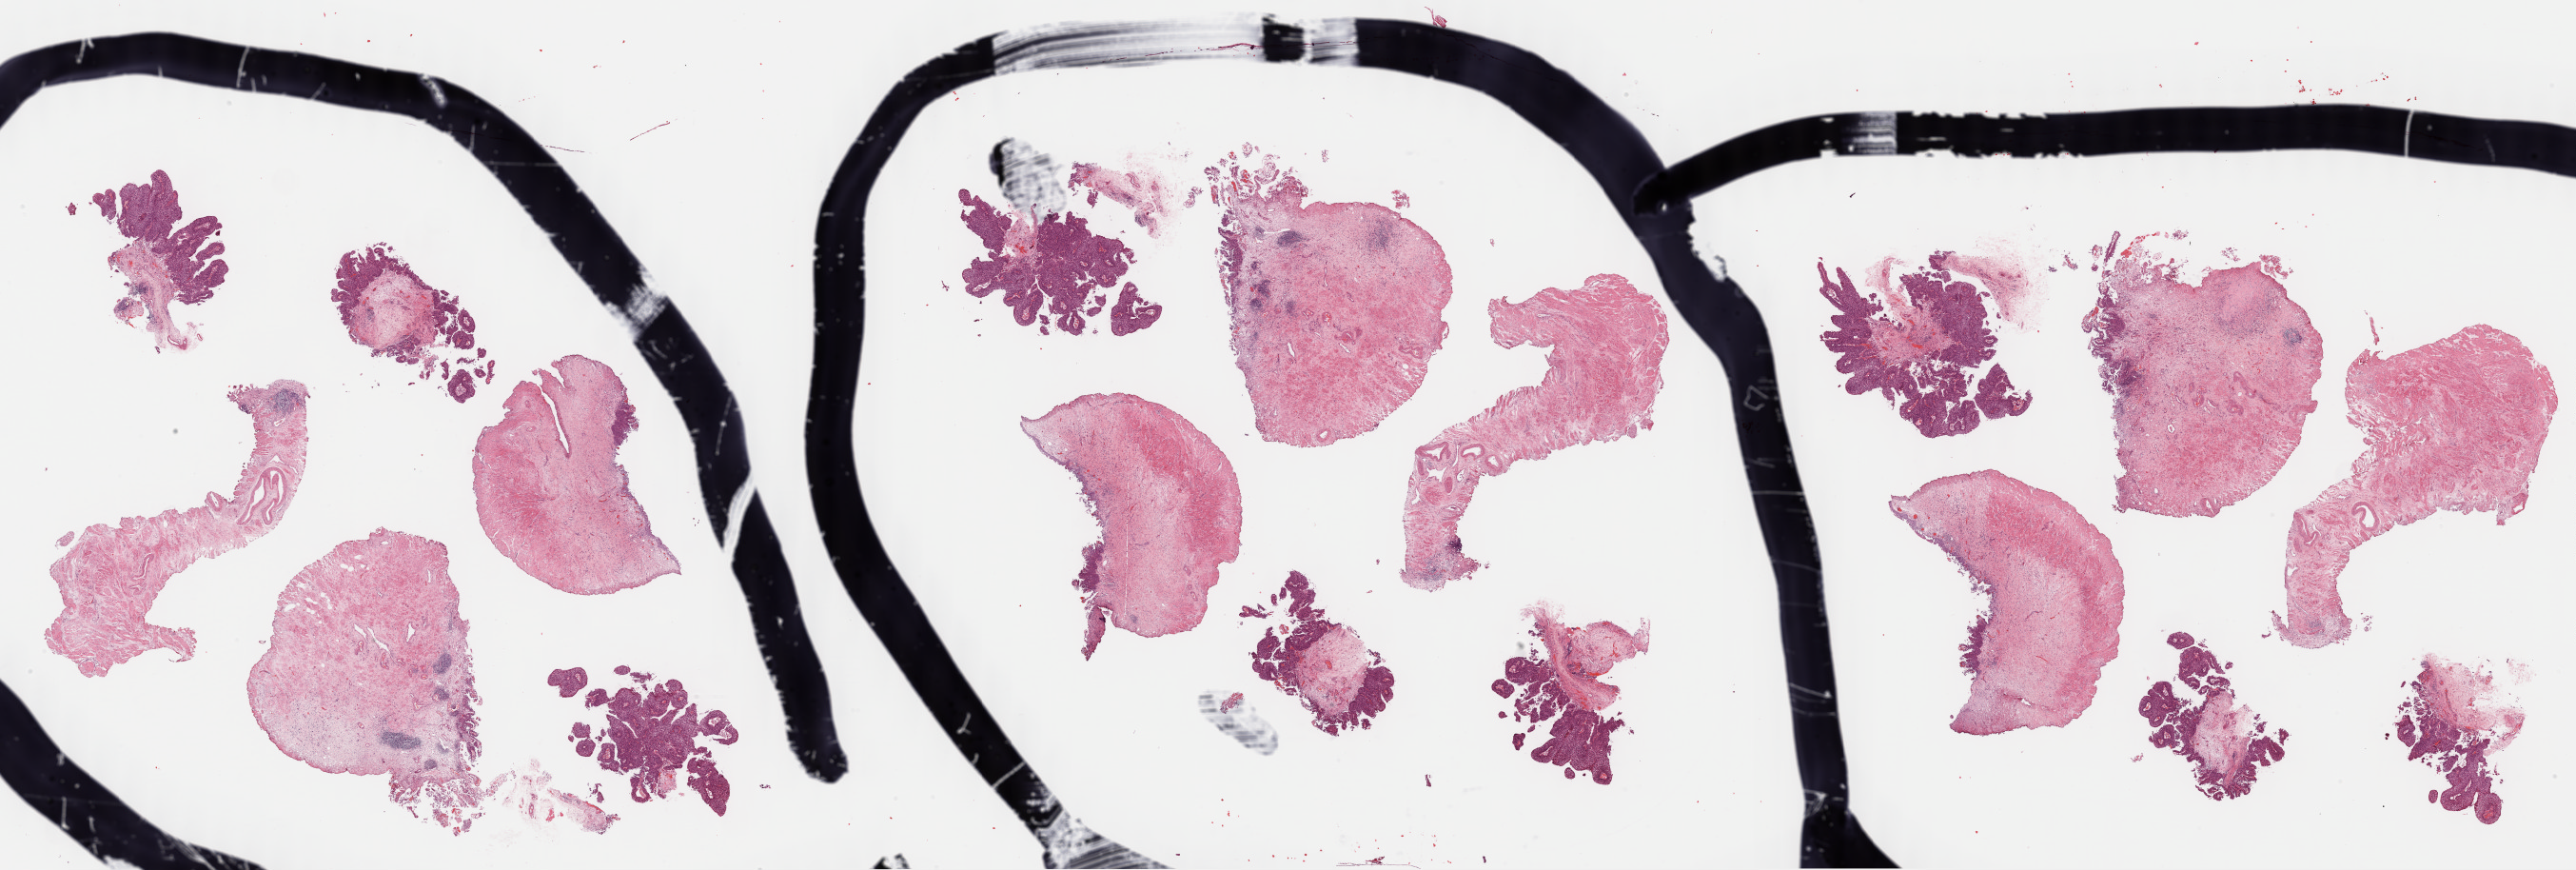
Whole-slide histology image, H&E — whole scanned area (about 43.8 x 14.8 mm, from a 40x scan) shown as a low-resolution overview; FFPE section; sample: primary tumour, bladder. Patient: male, age at initial diagnosis 61 years.
Diagnosis: Transitional cell carcinoma.